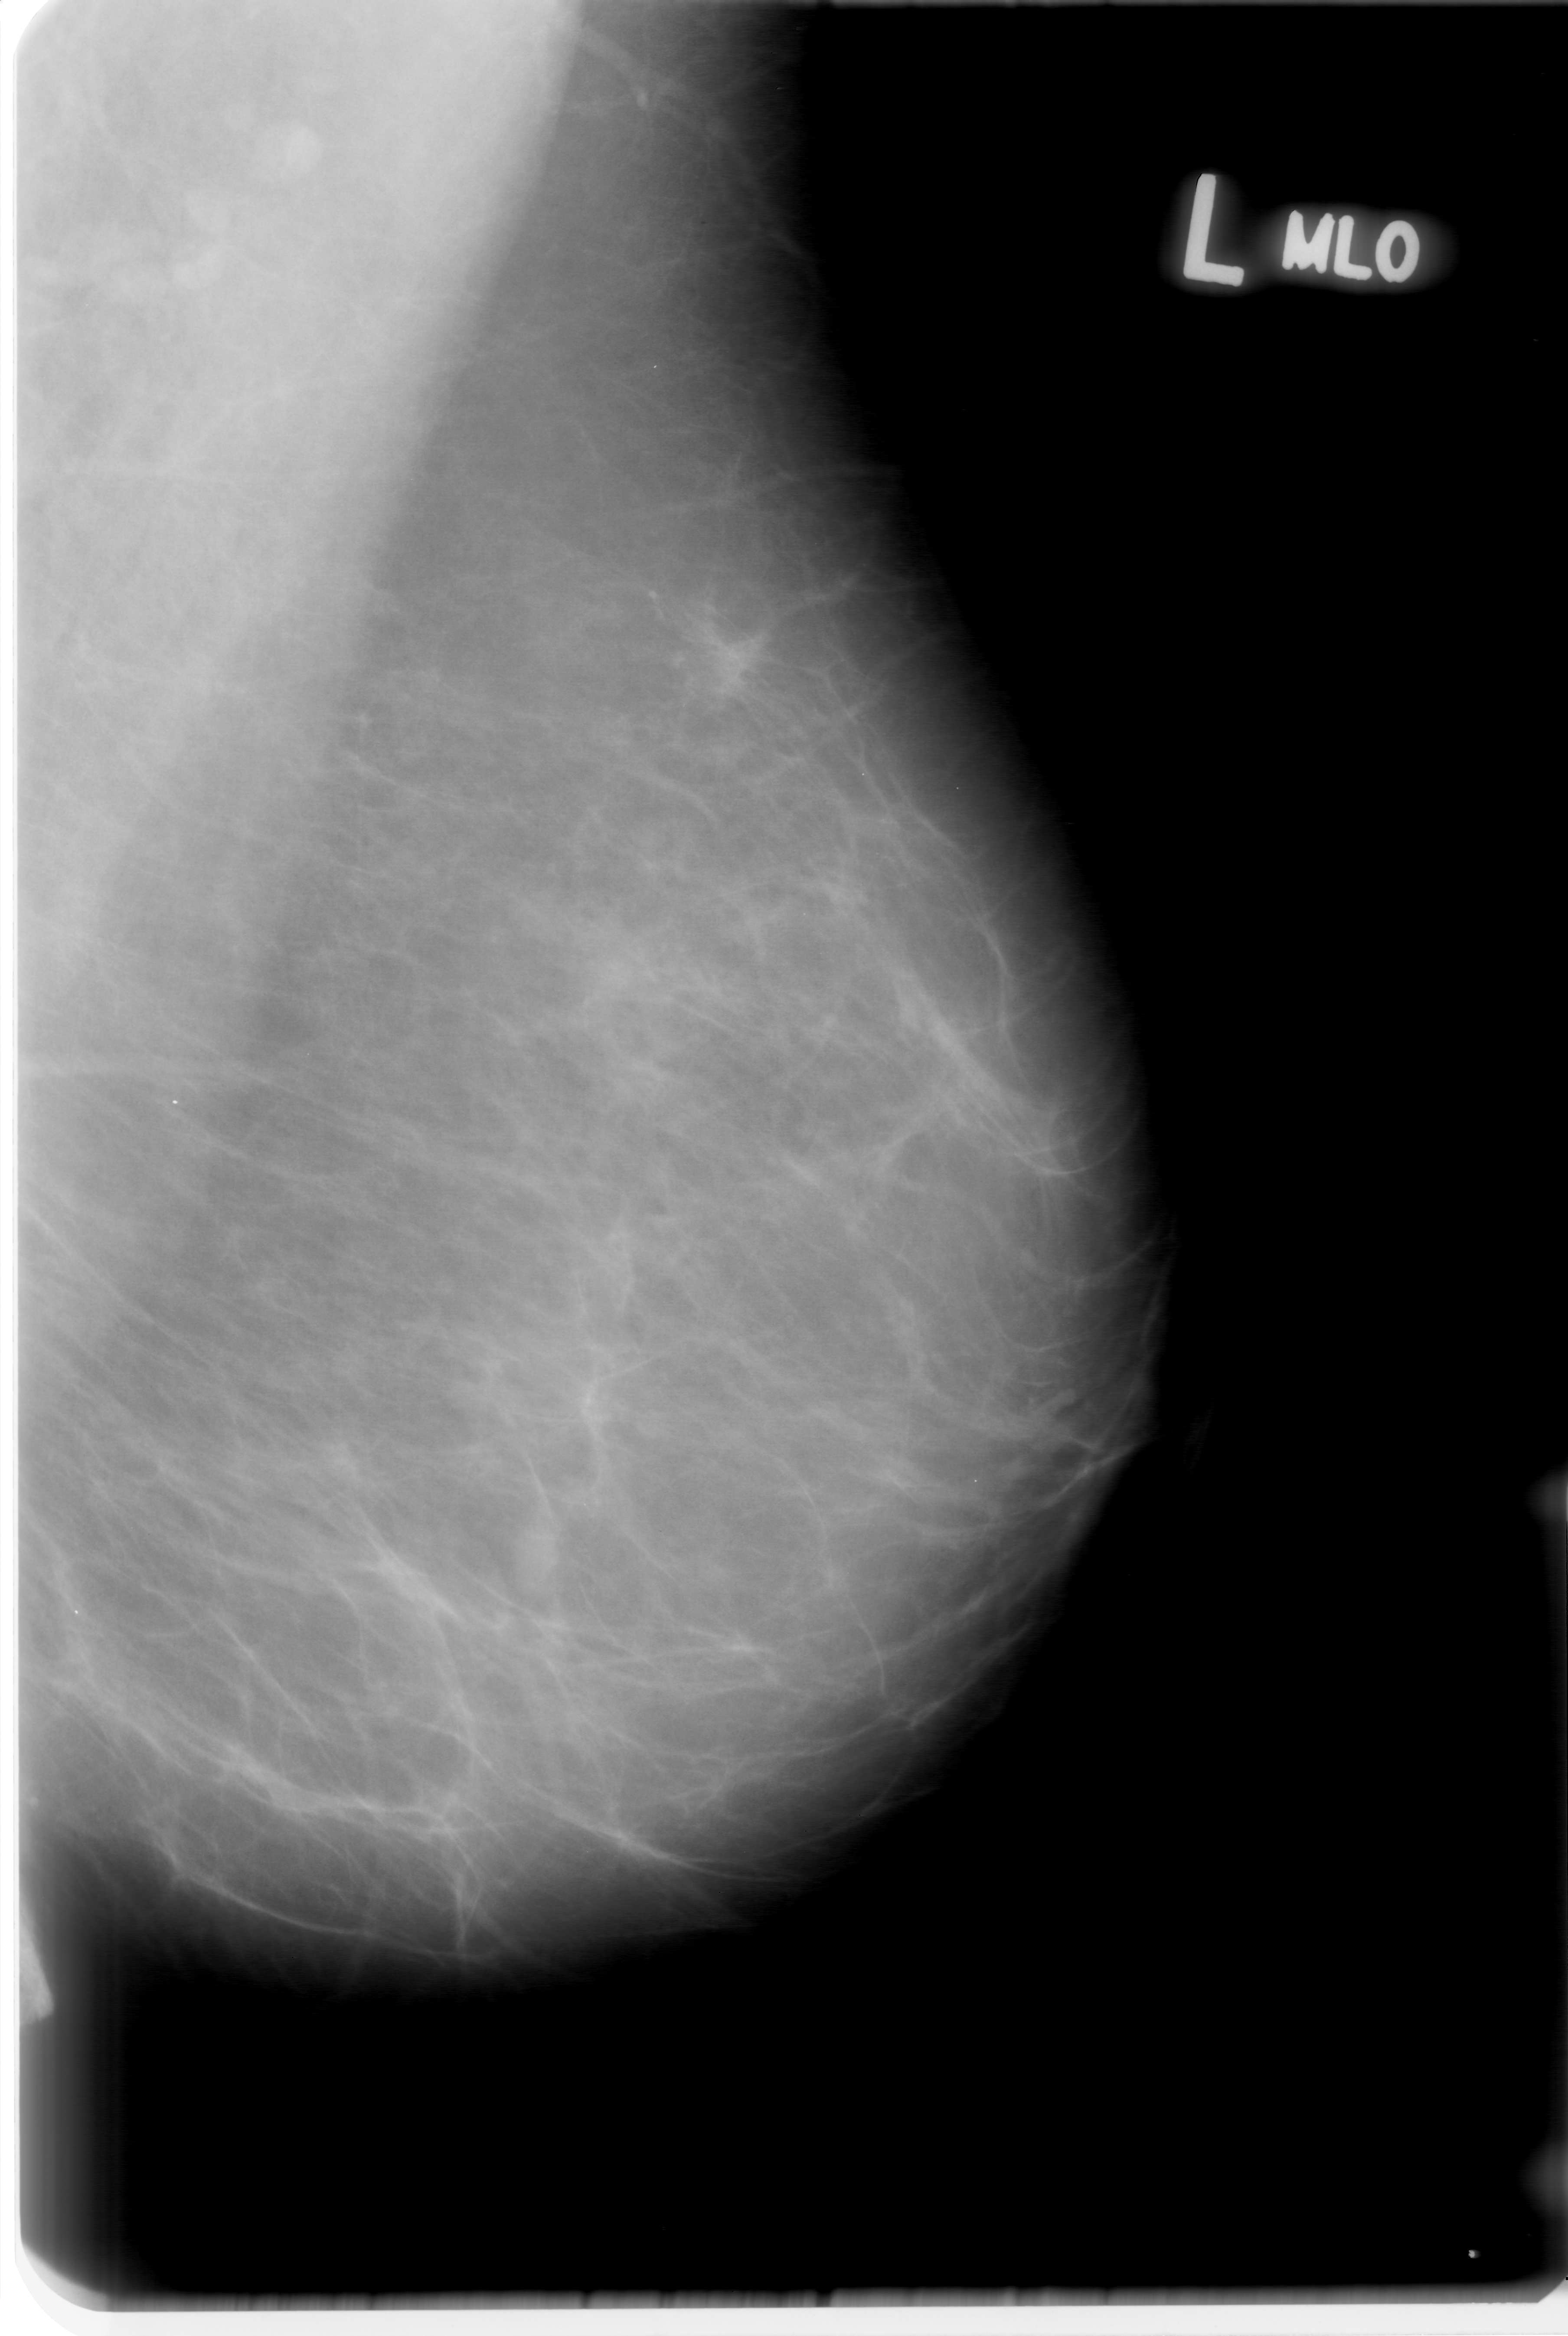
Mammogram (digitized film); left breast; mediolateral oblique (MLO) view; BI-RADS breast density category 1 (scale 1–4).
Finding: mass, shape oval, margins obscured; BI-RADS assessment category 0 (incomplete: needs additional imaging); pathology result (as recorded, not read from the image): benign.